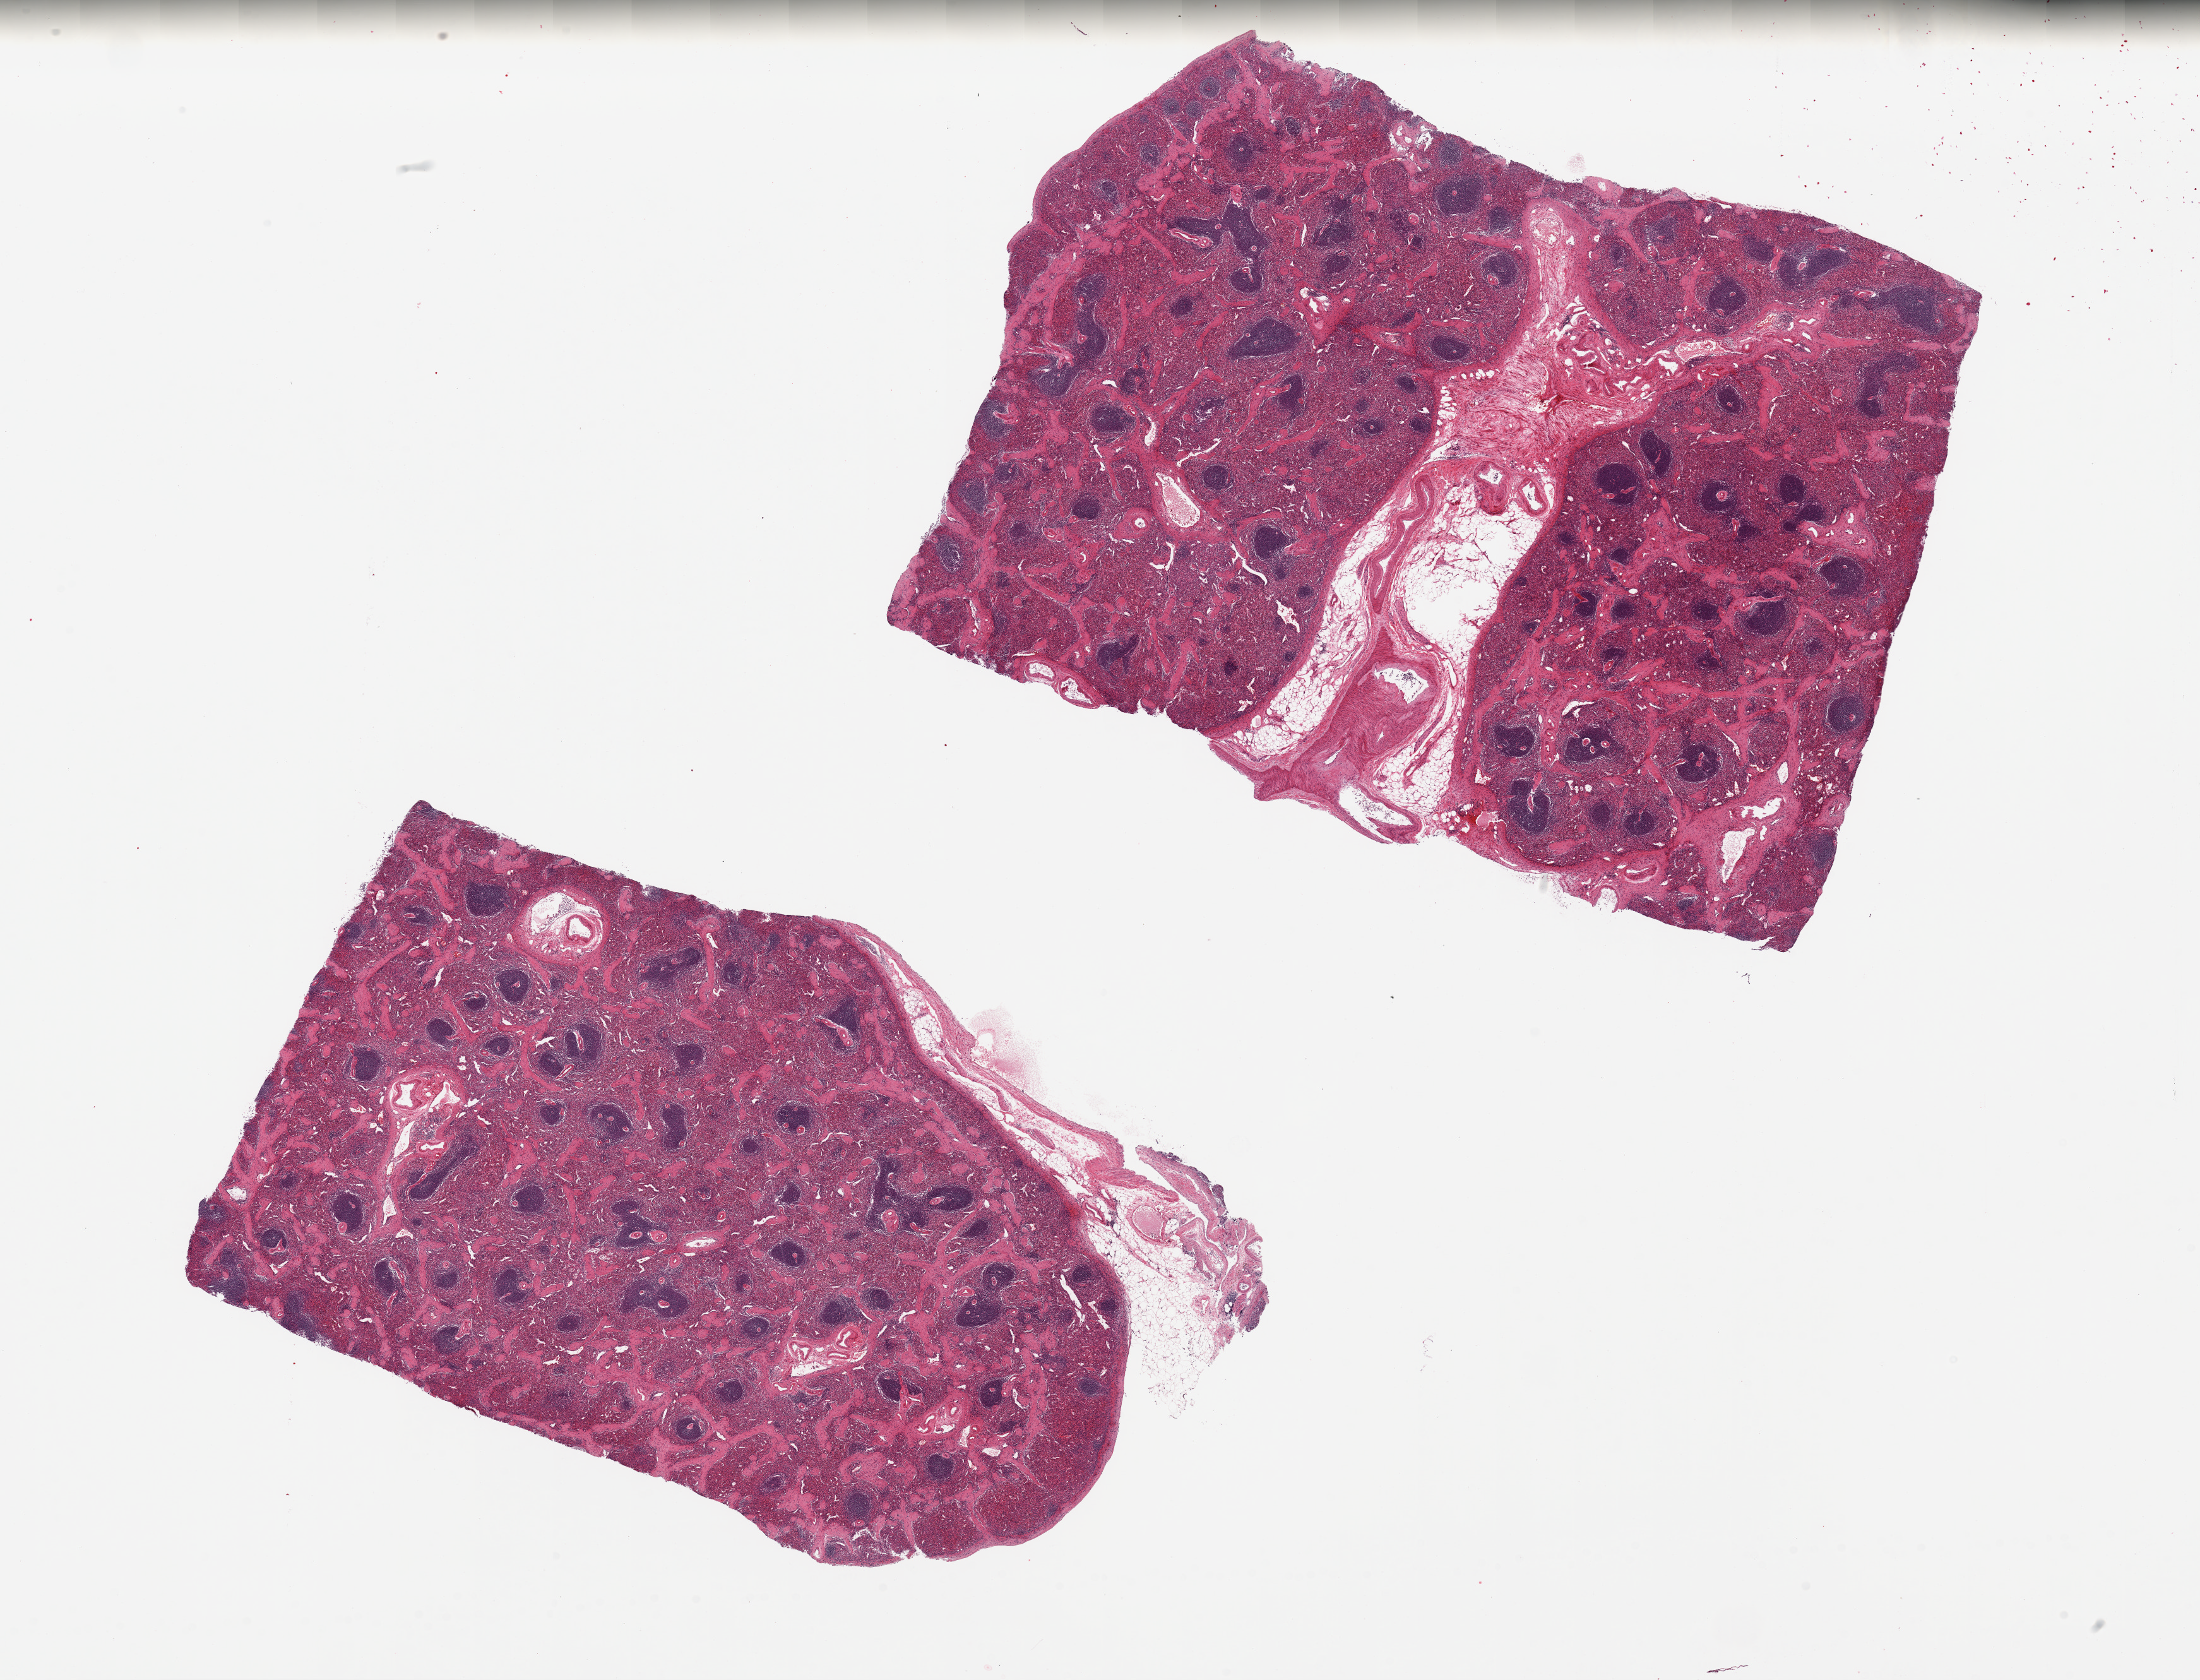
Hematoxylin and eosin (H&E) whole-slide image, brightfield, a low-resolution overview of the entire scanned area, about 27.6 x 21.0 mm, PAXgene-fixed, paraffin-embedded tissue, sampled site (target tissue): spleen, donor tissue sample.
- pathologist's review note for this sample: 2 pieces. Prominent vascular hyalinization